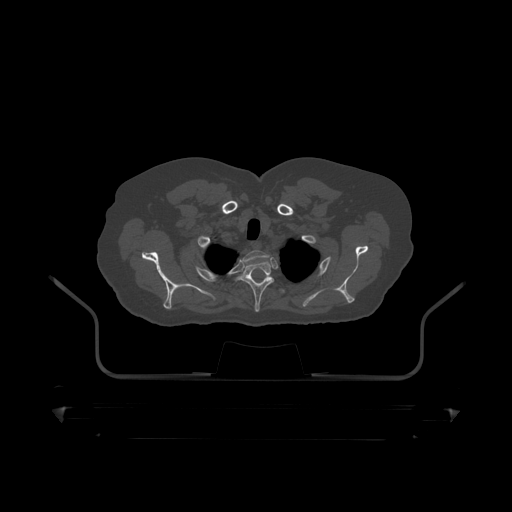
CT including the spine, one axial slice. Slice 375 of 390 in the series (ordered by position). Reconstruction kernel STANDARD. 120 kVp. Bone window (W 1800 / L 400 HU). 1.25 mm slice thickness. 512 × 512 image matrix. Male patient, age 60 years. Case-level facts recorded for this patient, not image findings: primary cancer: prostate.
Structures marked on this image (semi-automatically segmented with operator editing):
- T1 vertebra: box from (x=240, y=251) to (x=269, y=268) px
- T2 vertebra: (x=240, y=260)–(x=275, y=312)
- T3 vertebra: (x=249, y=276)–(x=286, y=295)